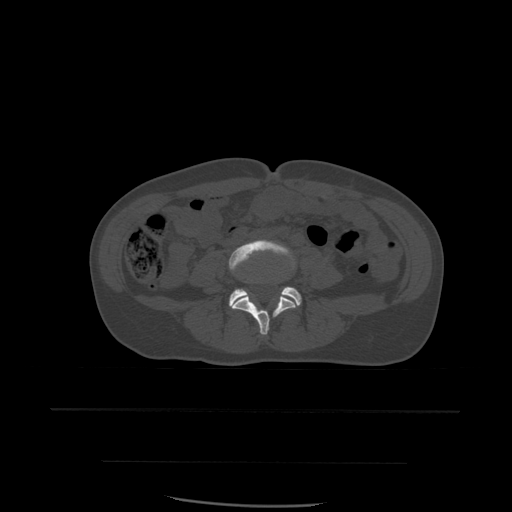
CT including the spine, one axial slice. Position 162 of 574 along the scan axis. Bone window (W 1800 / L 400 HU). 512 × 512 image matrix. Patient age 48 years. From the clinical record (not read from this slice): primary cancer: lung.
Annotated regions visible in this slice (semi-automatically segmented with operator editing):
- L4 vertebra: bounding box [x1, y1, x2, y2] px = [229, 240, 296, 336]
- L5 vertebra: [229, 287, 302, 308]